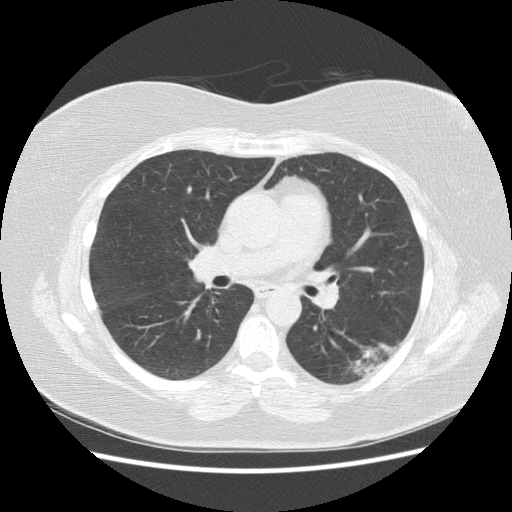
Low-dose screening chest CT, one axial slice. Position 86 of 151 along the scan axis. Lung window (W 1500 / L -600 HU). 2.5 mm slice thickness. 512 × 512 image matrix, field of view 360 × 360 mm.
Annotated regions visible in this slice (expert manual segmentation):
- lesion 1 (tumor, lower lobe of left lung): bounding box (x1, y1, x2, y2) in pixels: (352, 342, 401, 377)